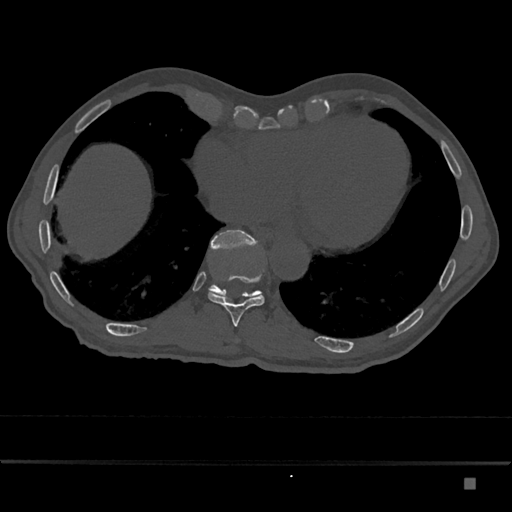
CT including the spine, one axial slice; position 726 of 797 along the scan axis; reconstruction kernel Br40s/3; 120 kVp; bone window (W 1800 / L 400 HU); 0.5 mm slice thickness; 512 × 512 image matrix, field of view 390 × 390 mm. Patient: male, 72 years. Case-level facts recorded for this patient, not image findings: primary cancer: prostate.
Annotated regions visible in this slice (semi-automatic segmentation, software-assisted and operator-edited):
- T10 vertebra: bounding box (x1, y1, x2, y2) in pixels: (208, 276, 265, 327)
- T11 vertebra: (208, 230, 262, 299)